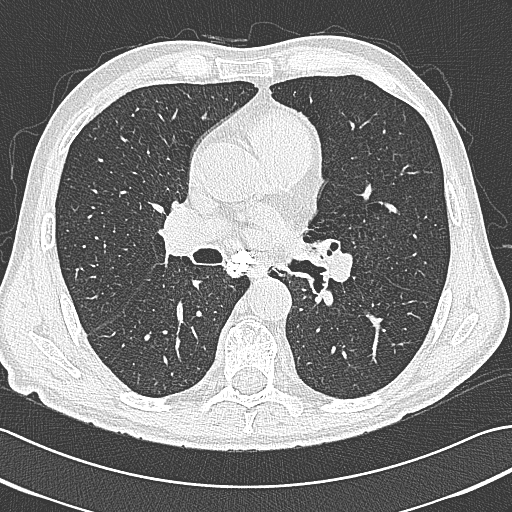
Low-dose screening chest CT, axial slice. Baseline screening round. Lung window (W 1500 / L -600 HU). Slice 177 of 380 in the series. Male, age 65 years at enrolment. Current smoker at enrolment.
Expert-annotated lung lesion, bounding box (x1, y1, x2, y2) in pixels: (304, 231, 349, 277). Screening reader's record for this exam: no non-calcified nodule ≥4 mm recorded. Official screen result: negative screen, minor abnormalities not suspicious for lung cancer.